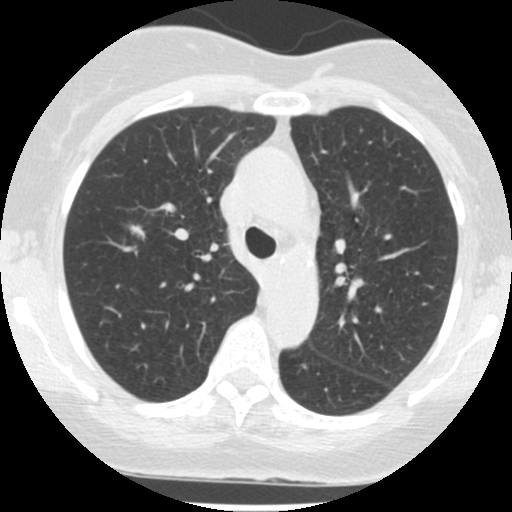
Axial slice from a low-dose chest CT screening exam. Second annual screen. Lung window (W 1500 / L -600 HU). 2.5 mm slice thickness. Standard (soft-tissue) reconstruction kernel (STANDARD). 120 kVp. Female participant, aged 62 years at enrolment.
• Lesion marked by an expert reader, box from (x=109, y=210) to (x=160, y=253) px.
• The exam's reader record, not a measurement of the box and not confirmed to be the same lesion: non-calcified nodule or mass ≥4 mm, right upper lobe, 10 × 6 mm, spiculated (stellate) margins, soft tissue attenuation, pre-existing on the prior screen: yes; interval growth: yes.
• Official screen result: positive, other.
• Participant outcome: lung cancer diagnosed 515 days after this screen (after the third annual screen) — adenocarcinoma, NOS, right upper lobe, well differentiated (G1), stage IA (AJCC 6th edition), 7 mm at pathology.